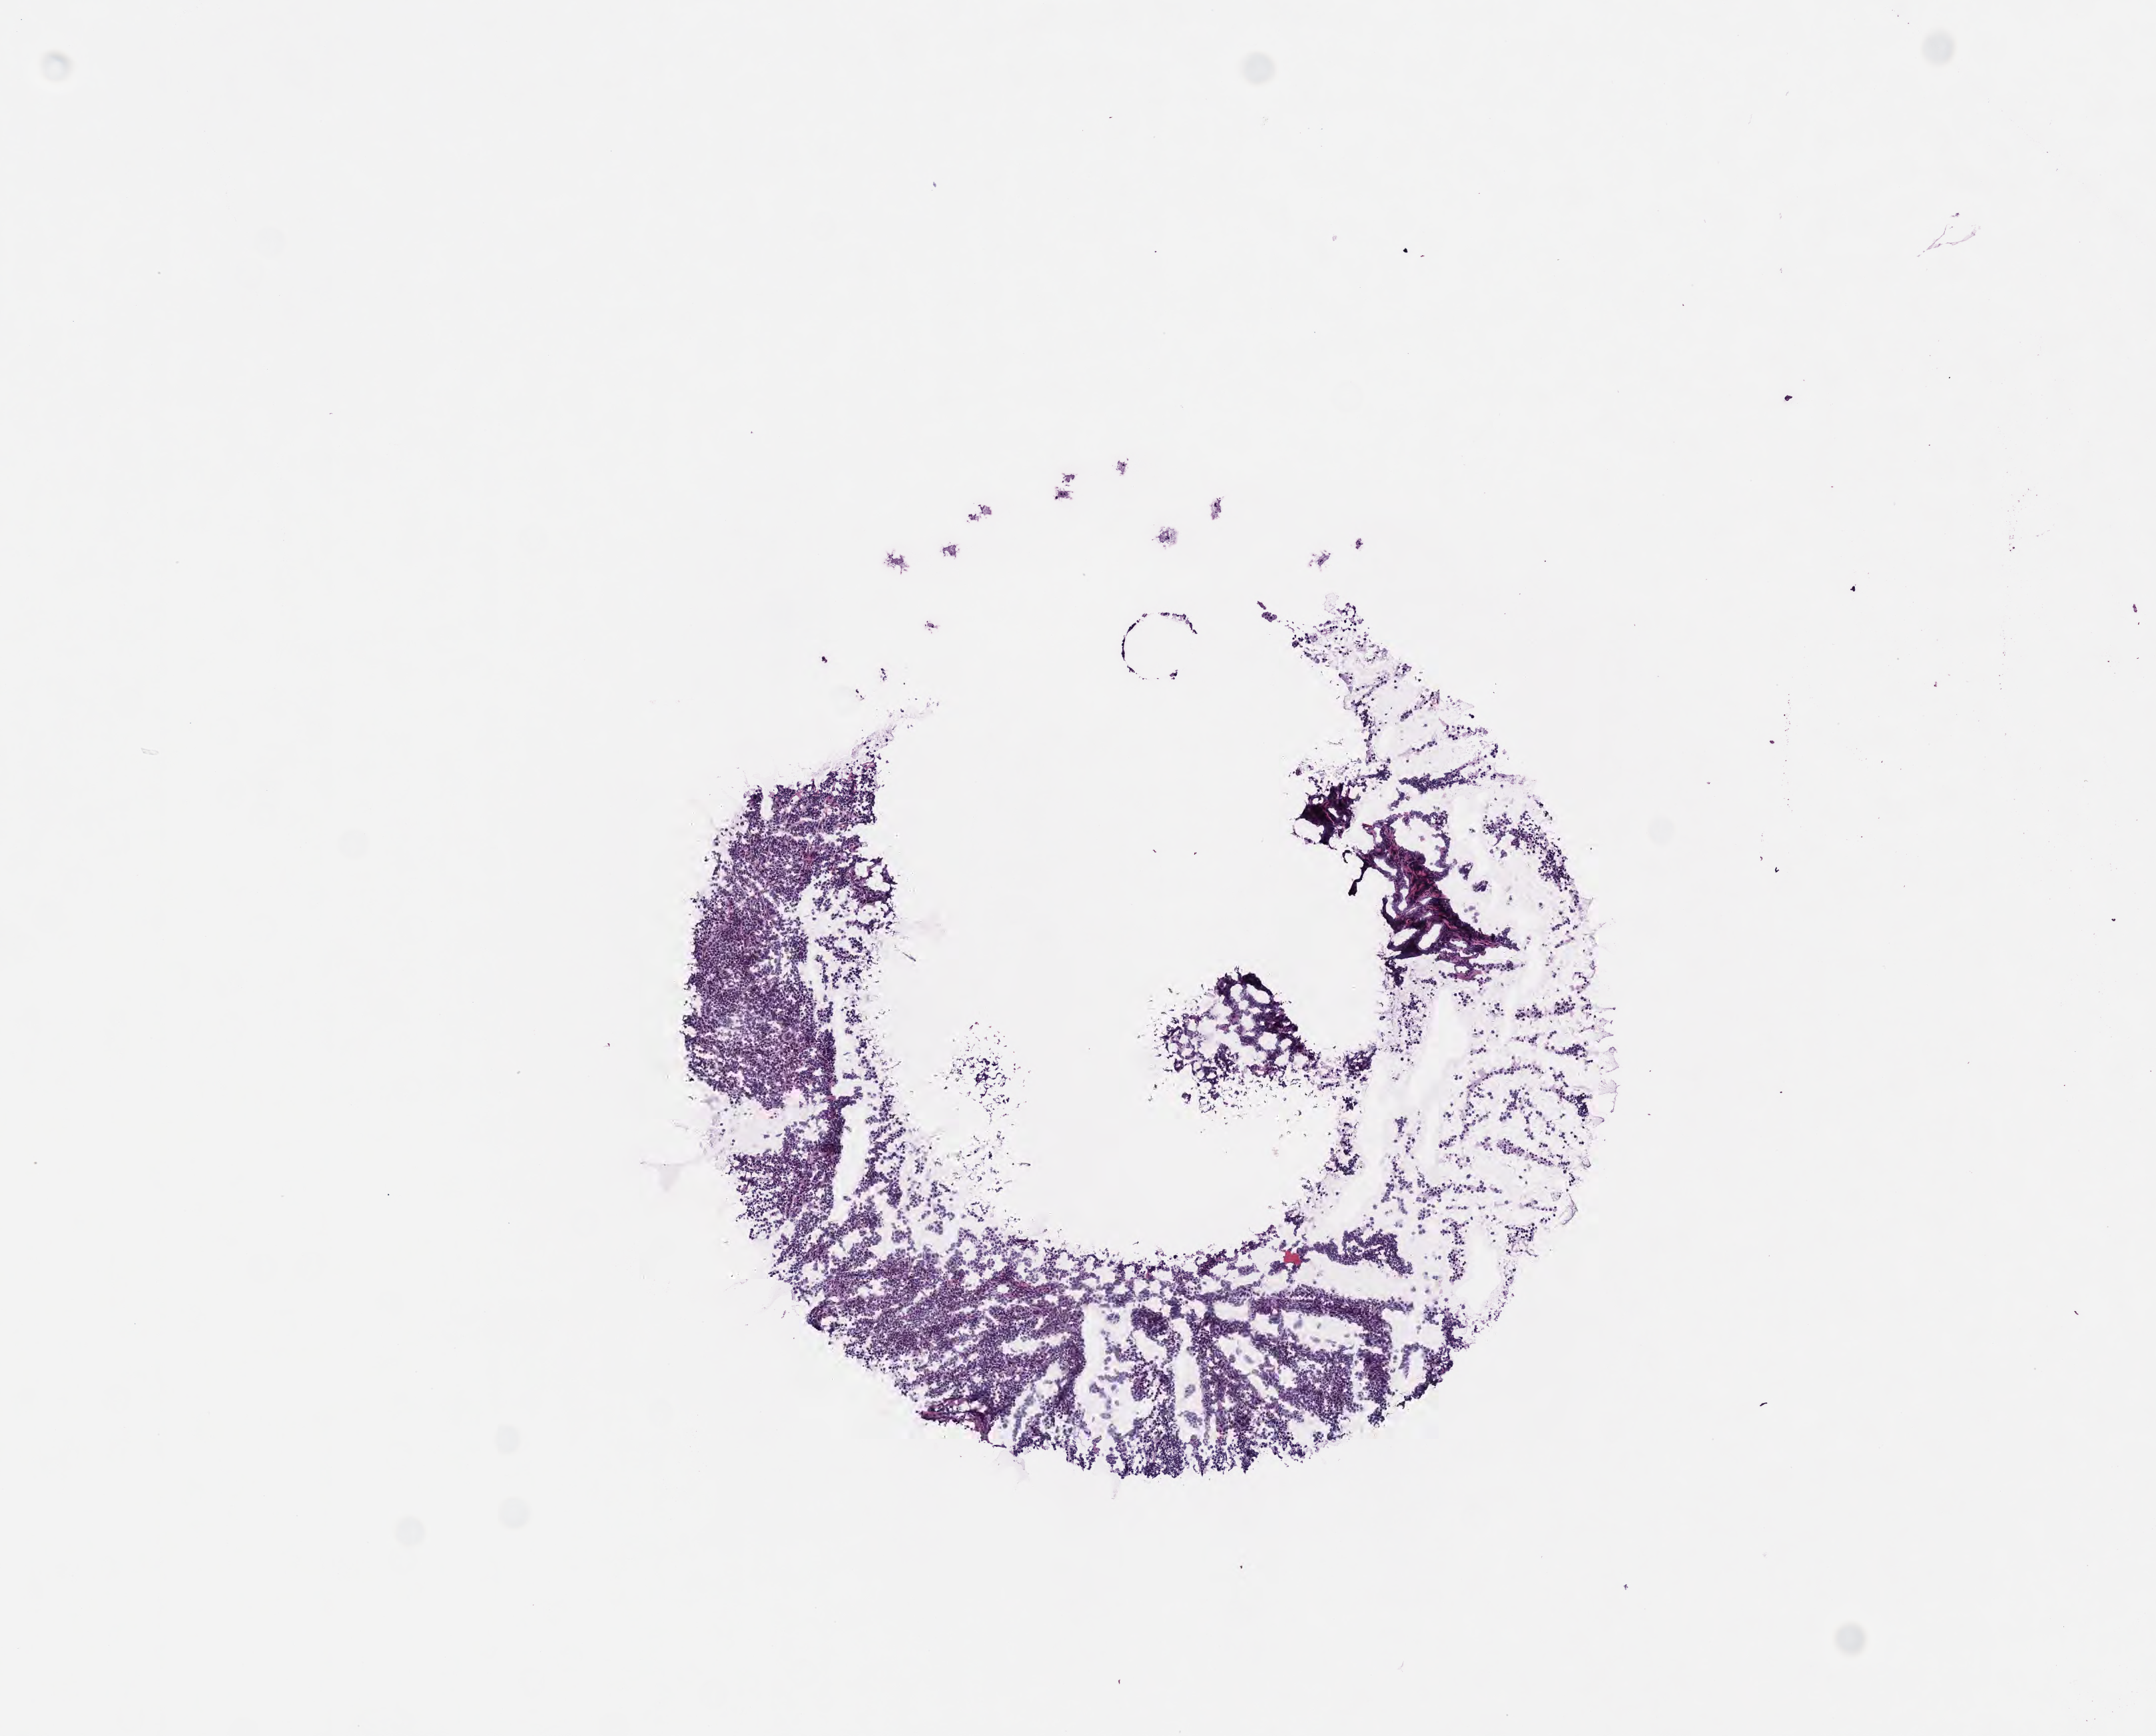
H&E whole-slide image — a low-resolution overview of the entire scanned area, about 6.5 x 5.3 mm, frozen section (tissue freezing medium), specimen: primary tumor, site: peritoneum. Female patient; age at initial diagnosis 7 years. Composition of this section per pathologist review: tumor cells 85%, tumor nuclei 90%, stromal cells 5%, necrosis 5%, normal cells 5%. Infiltration values recorded for this section: lymphocyte infiltration 10%, monocyte infiltration 20%, neutrophil infiltration 25%.
Section: top of the tissue portion. Diagnosis: Burkitt lymphoma, NOS. Ann Arbor stage (patient): Stage III.